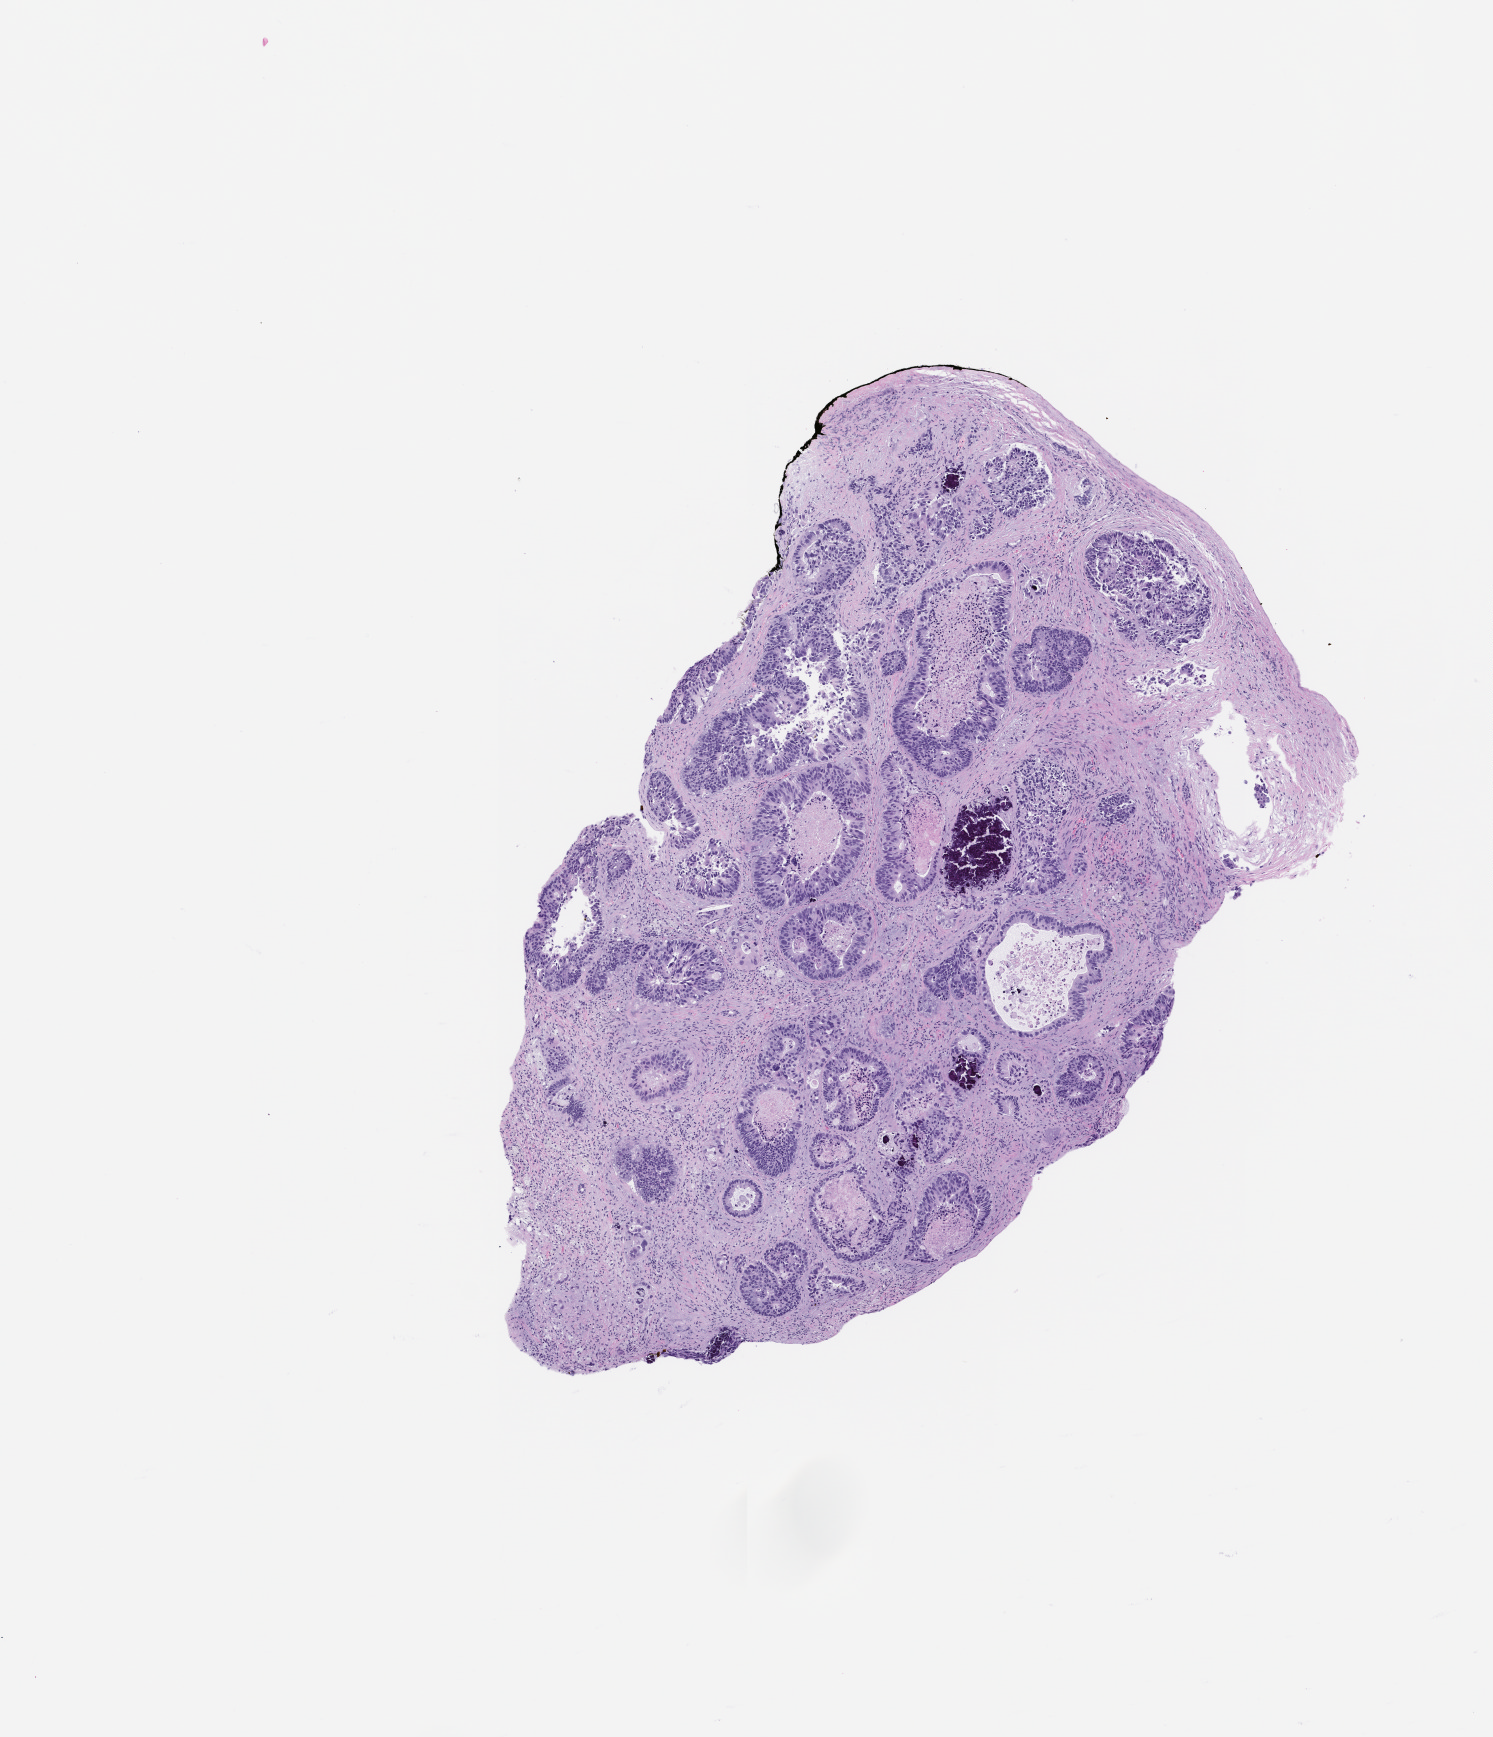
Whole-slide image, H&E stain of the patient's (originator) tumor tissue — a low-resolution overview of the entire scanned area, about 6.0 x 7.0 mm. Formalin-fixed, paraffin-embedded (FFPE) tissue. Tumor site category: colon. Patient: male.
• diagnosis: Colon Adenocarcinoma